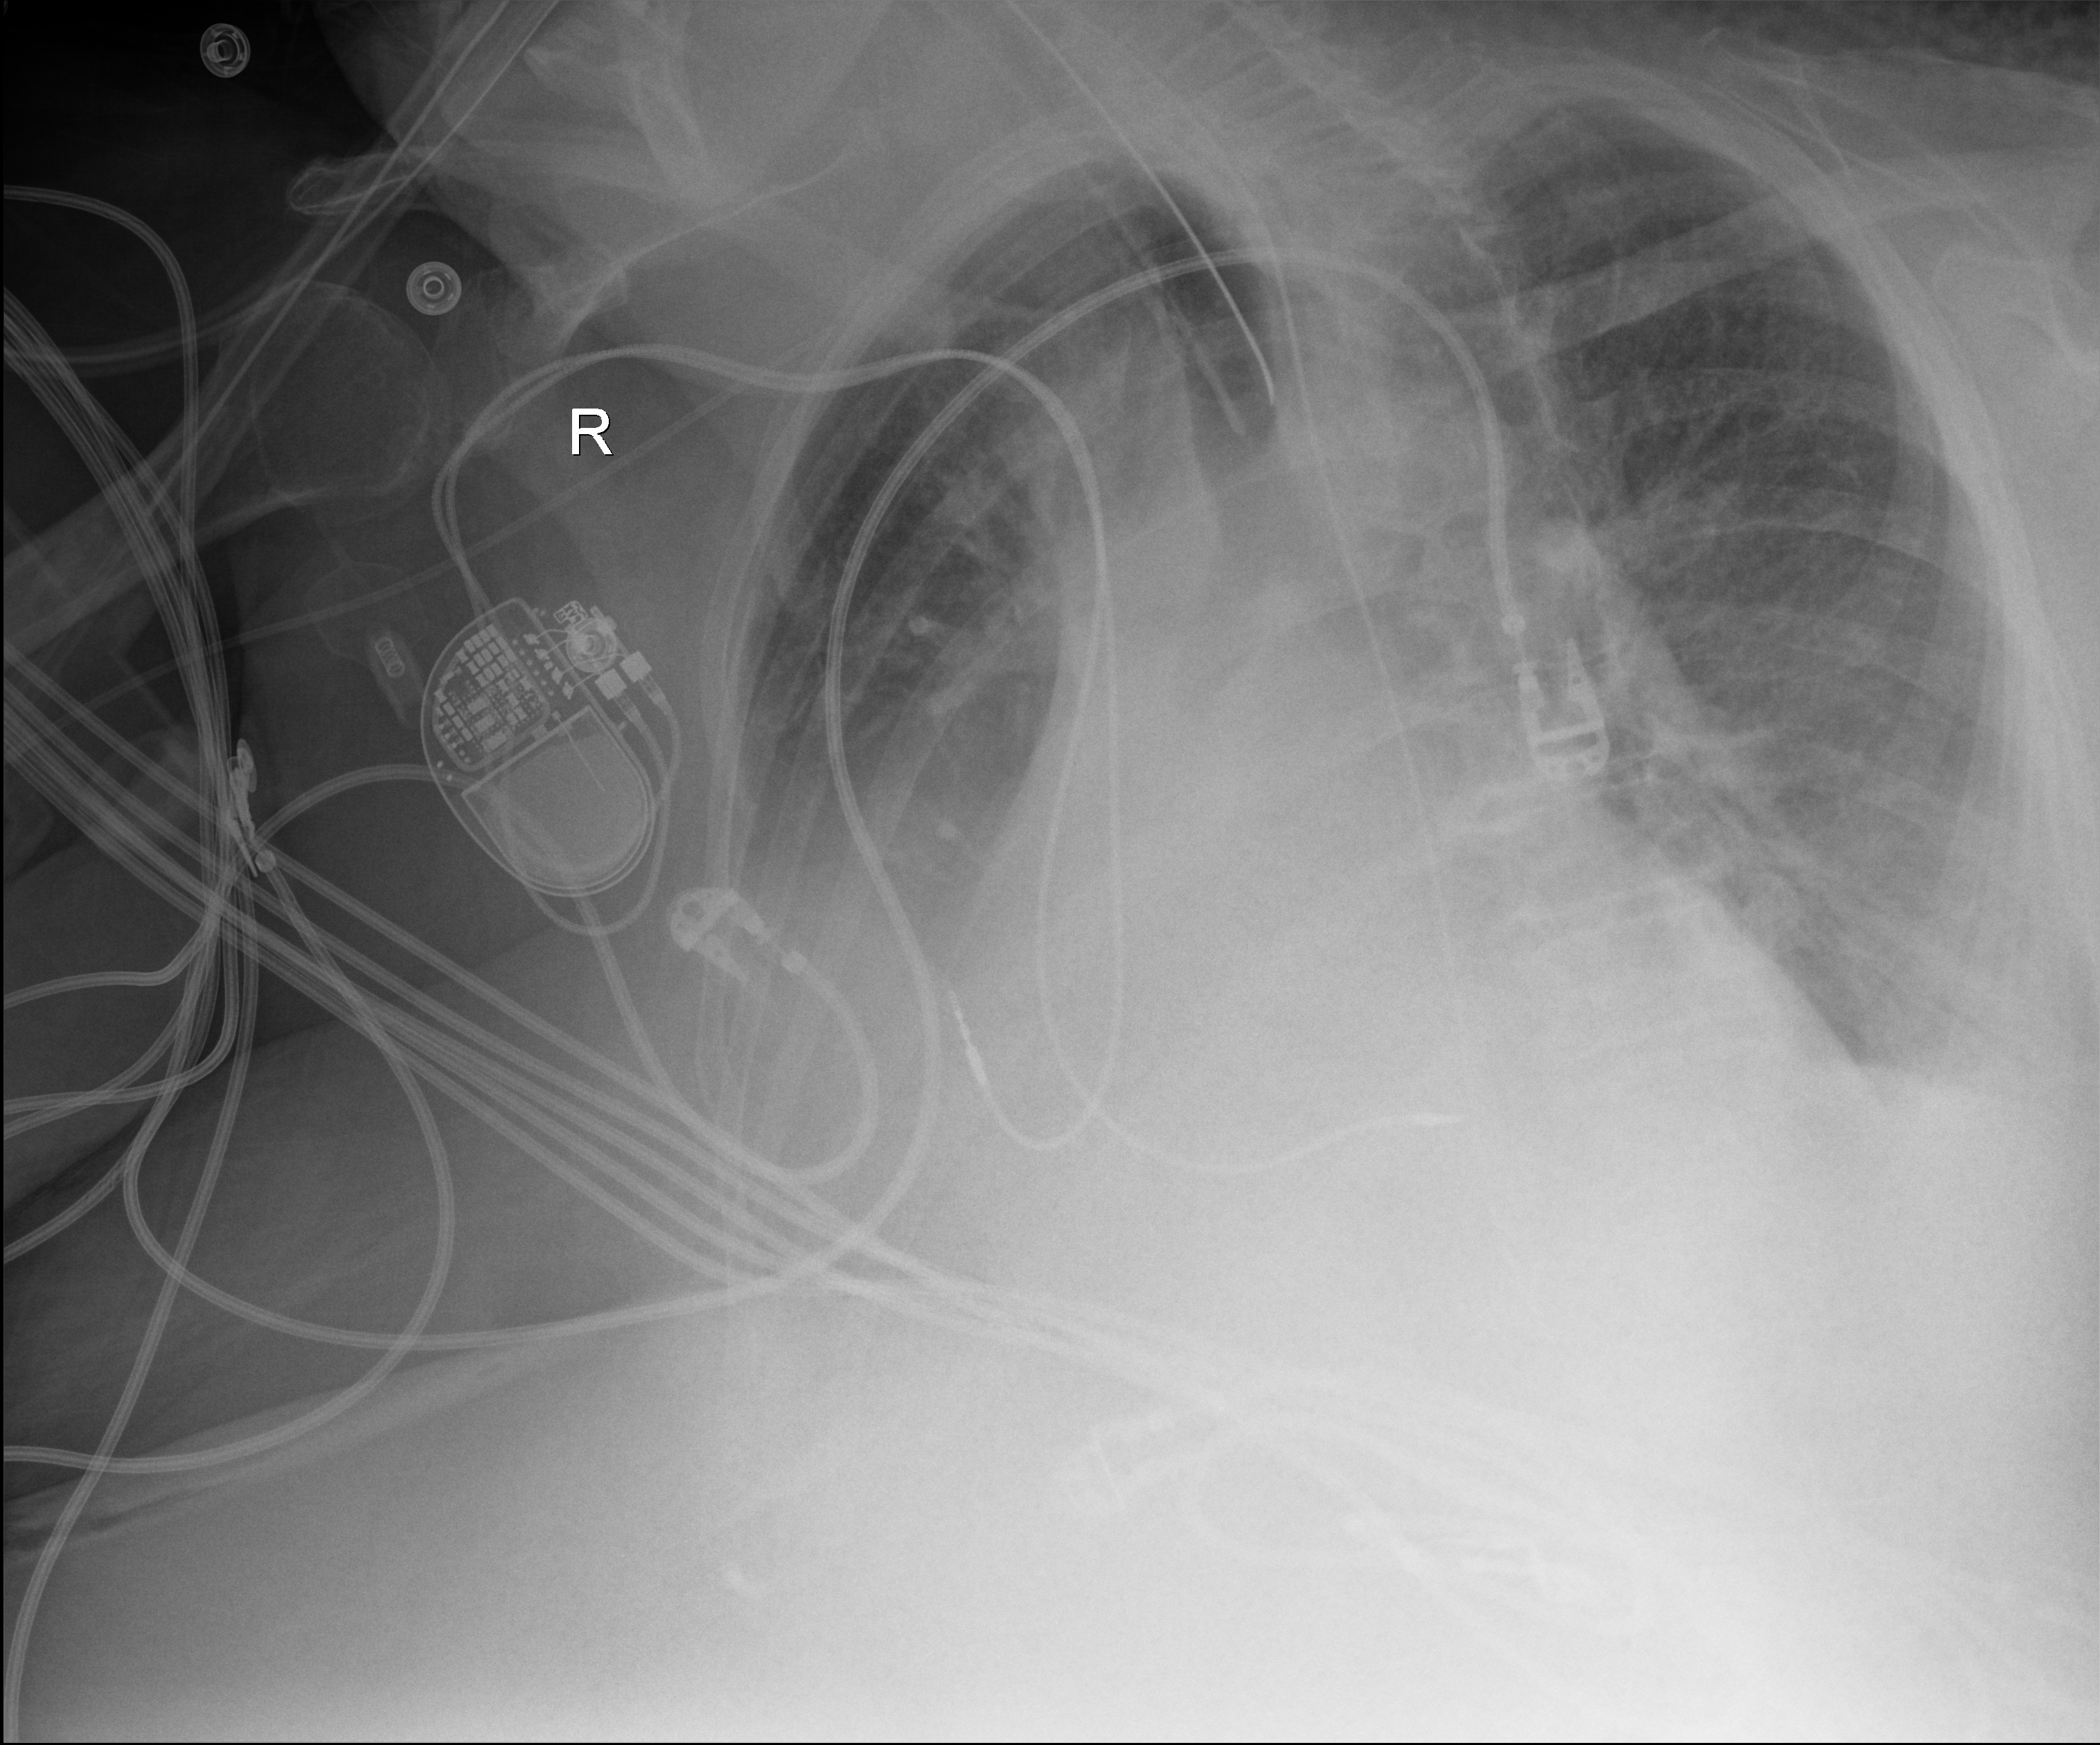
Chest X-ray (portable); anteroposterior (AP) projection. Patient hospitalised with COVID-19; female, aged 75–90 years.
Admission-level facts for this patient (not findings on this image; timing relative to this image not recorded): admitted to intensive care during this hospital stay: yes; COPD (admission record): yes.